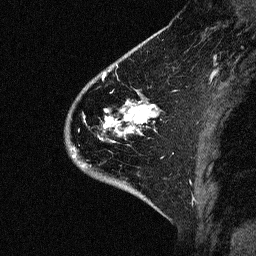
Breast MRI (dynamic contrast-enhanced), one sagittal slice; dynamic contrast-enhanced study with each time point stored as its own series, time point 2 of 3 at this slice position (early post-contrast, ordered by acquisition time); 1.5 T; TE 4.5 ms, TR 11 ms; 256 × 256 image matrix, field of view 200 × 200 mm. Female patient, age 46 years. From the clinical record (not read from this slice): setting: breast cancer imaged before/during neoadjuvant chemotherapy; receptor status: HER2-positive.
Structures marked on this image (semi-automatic segmentation, software-assisted and operator-edited):
- analysis volume of interest (the breast-tissue region the enhancement analysis was run in; not a lesion): bounding box [x1, y1, x2, y2] px = [44, 72, 176, 177]
- tumour enhancement mask (voxels above the 90 % enhancement threshold inside the analysis volume of interest): [100, 74, 155, 140]